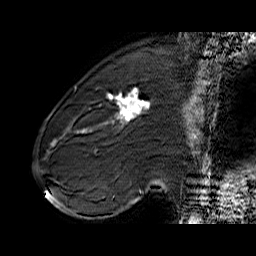
Breast MRI (dynamic contrast-enhanced), one sagittal slice; dynamic contrast-enhanced series, time point 2 of 6 at this slice position (early post-contrast); 1.5 T; TE 6.4 ms, TR 32.9 ms; 4 mm slice thickness; 256 × 256 image matrix, field of view 200 × 200 mm. Female patient. From the clinical record (not read from this slice): setting: breast cancer imaged before/during neoadjuvant chemotherapy; receptor status: HER2-positive.
Outlined on this slice (semi-automatic segmentation, software-assisted and operator-edited):
- analysis volume of interest (the breast-tissue region the enhancement analysis was run in; not a lesion): bounding box [x1, y1, x2, y2] px = [71, 80, 155, 146]
- tumour enhancement mask (voxels above the 100 % enhancement threshold inside the analysis volume of interest): [77, 88, 150, 132]